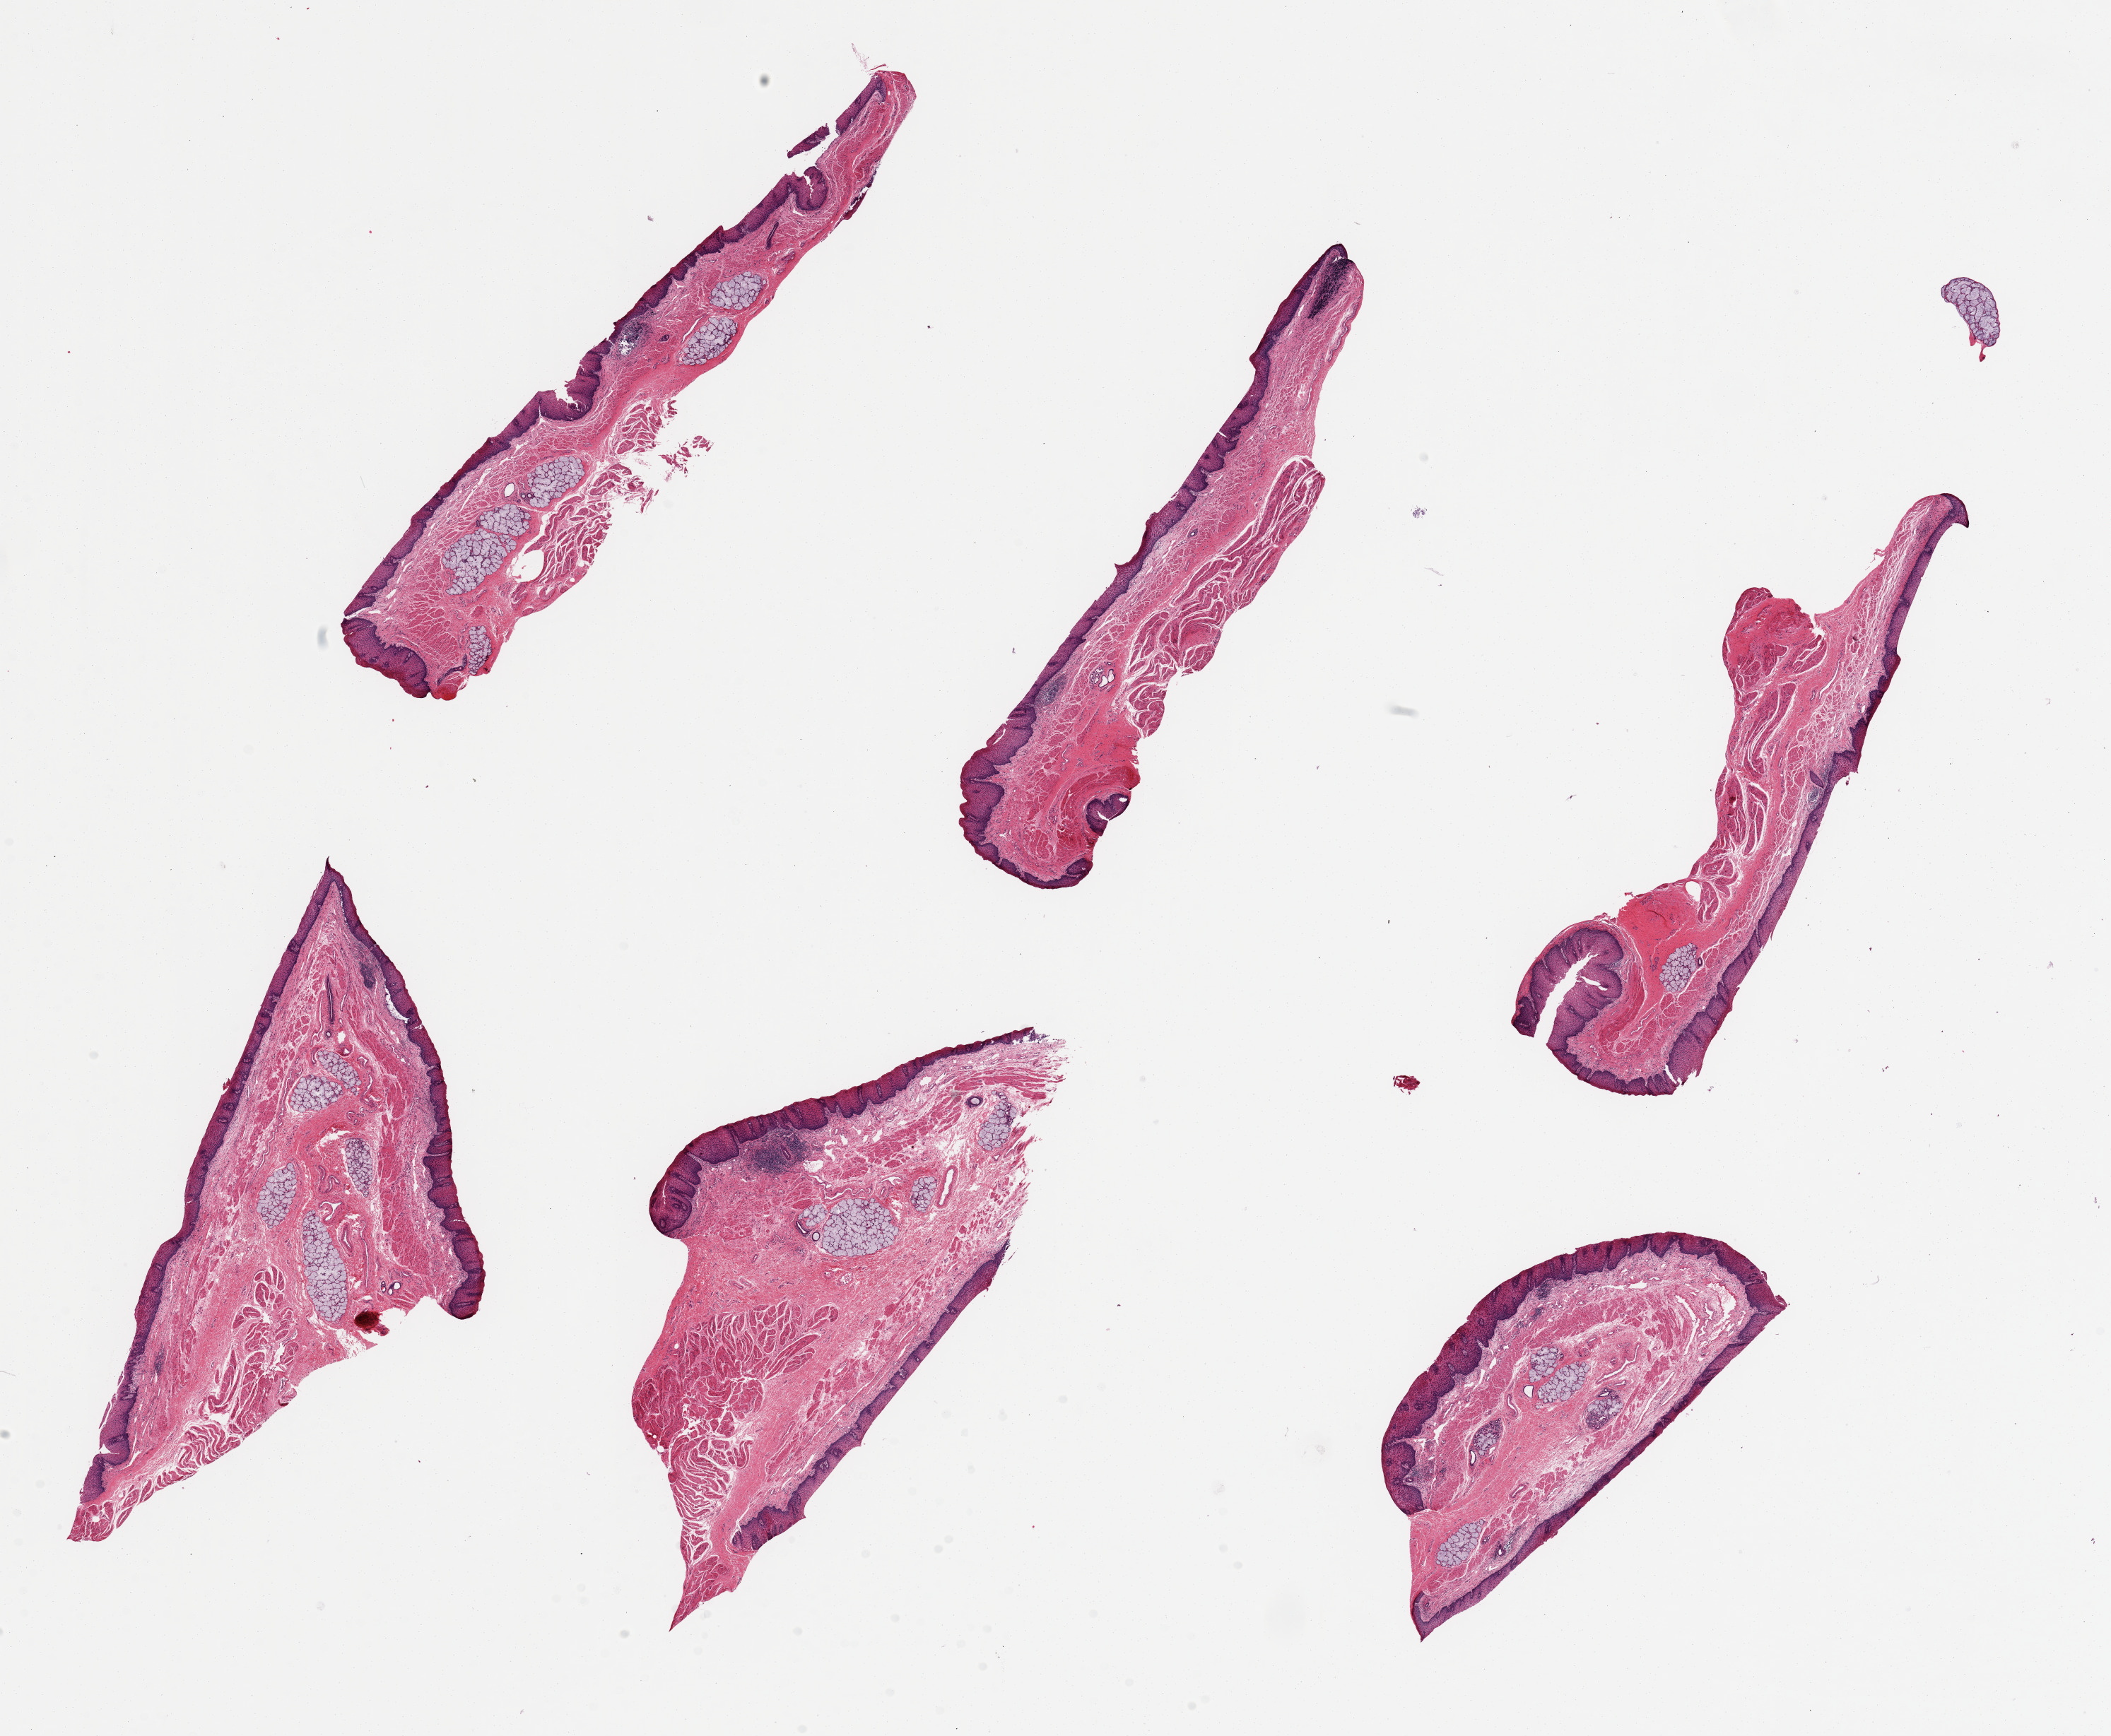
Whole-slide image, hematoxylin and eosin (H&E) stain — shown as a low-resolution overview of the whole scanned area (about 23.6 x 19.4 mm), PAXgene-fixed paraffin-embedded (PFPE) section, sampled site (target tissue): esophageal mucous membrane, donor tissue sample. Female donor.
Pathologist's review note for this sample: 6 pieces up to 8x3.5 mm; all have mucosa and abundant submucosal glands.